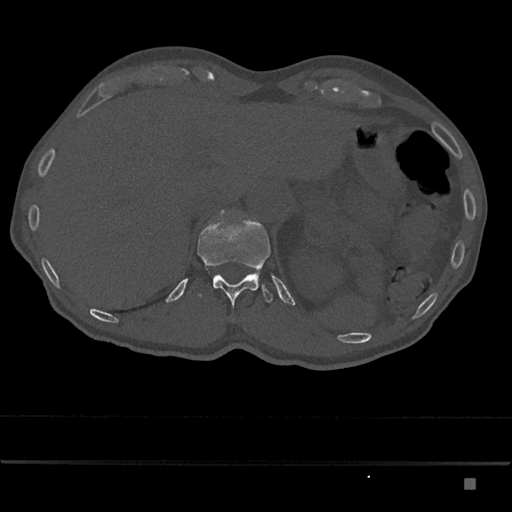
CT including the spine, one axial slice. Position 609 of 797 along the scan axis. Bone window (W 1800 / L 400 HU). 512 × 512 image matrix, field of view 390 × 390 mm. Male patient, age 72 years. From the clinical record (not read from this slice): primary cancer: prostate.
Structures marked on this image (semi-automatically segmented with operator editing):
- T12 vertebra: bounding box <197,216,273,307> (left, top, right, bottom; pixels)